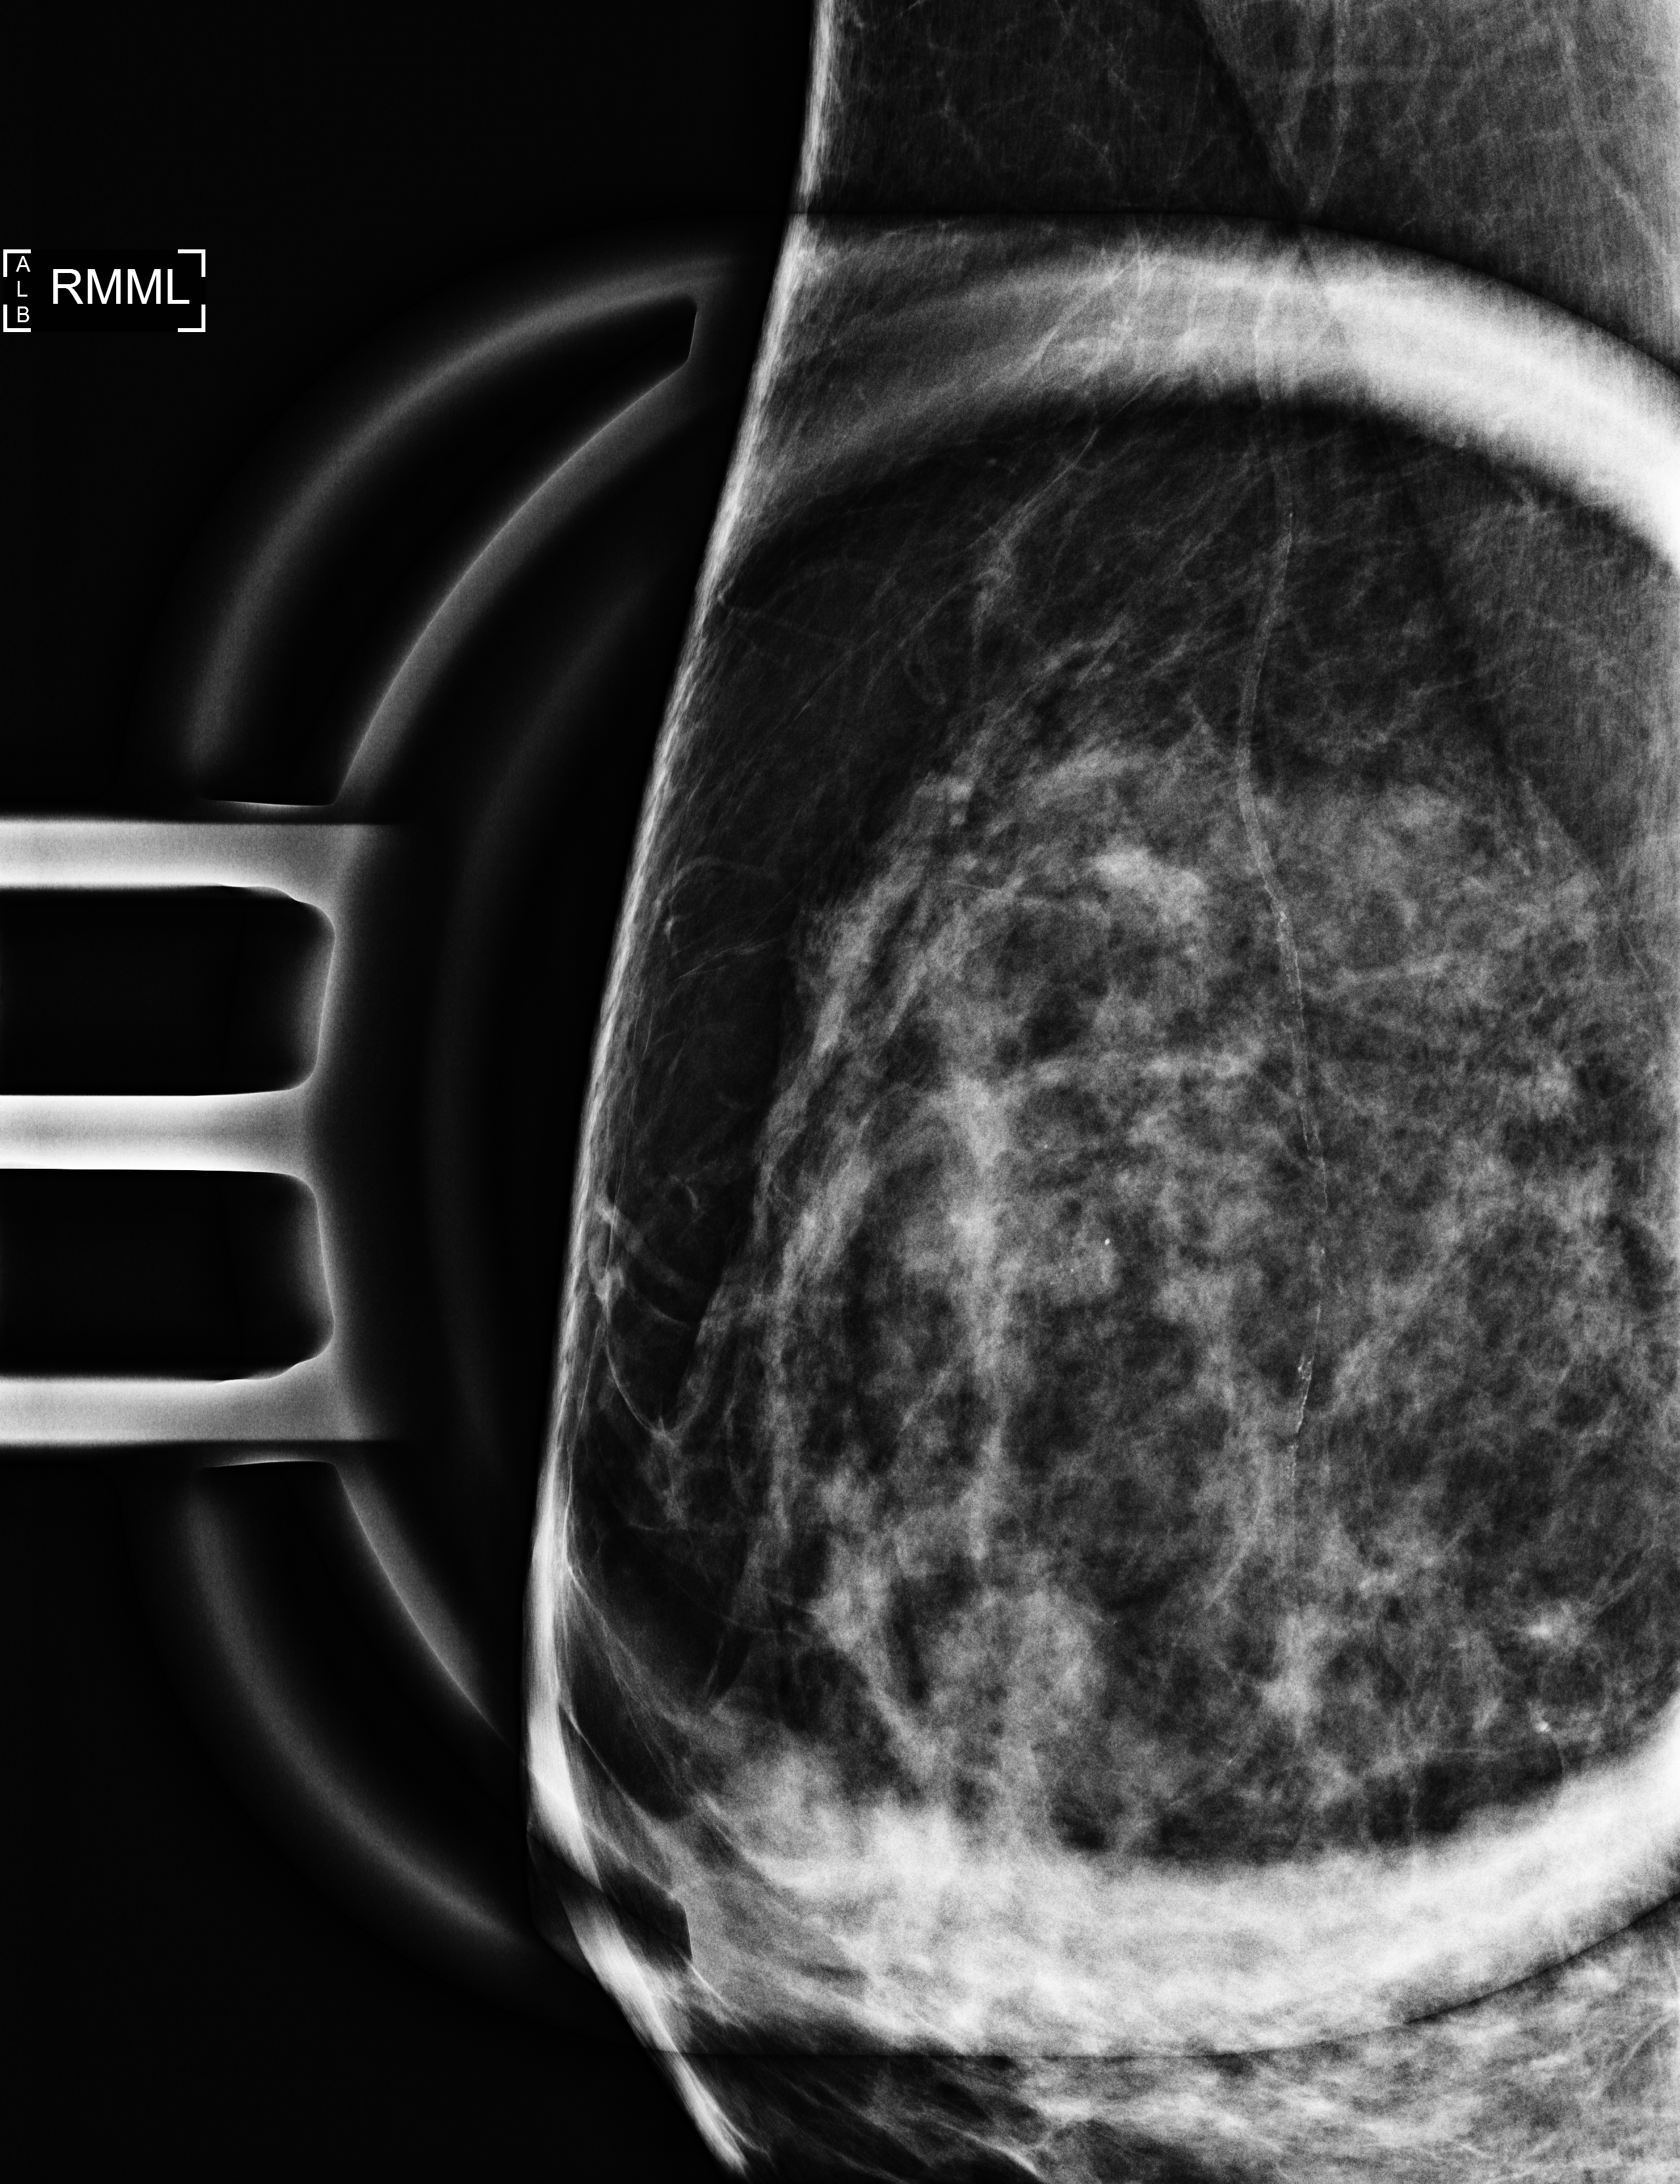
Additional (diagnostic) view; compressed breast thickness 47 mm. Patient: female, 55 years.
Image type: full-field digital mammogram. Breast: right. Projection: mediolateral (ML) view, magnification.